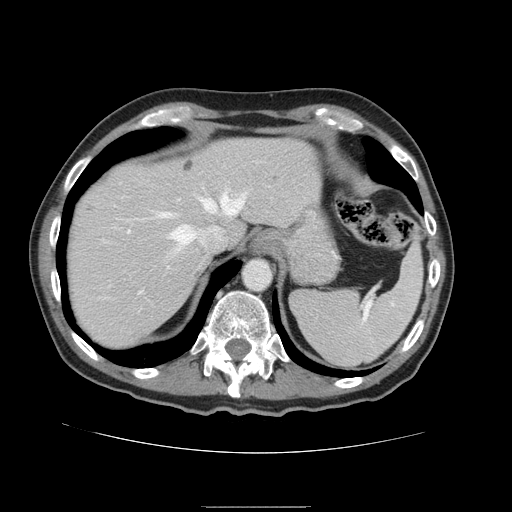
Contrast-enhanced abdominal CT, one axial slice; slice 122 of 168 in the series (ordered by position); soft-tissue window (W 400 / L 40 HU); 512 × 512 image matrix, field of view 386 × 386 mm. Male patient, age 74 years. Case-level facts recorded for this patient, not image findings: diagnosis: colorectal cancer liver metastases, imaged before liver resection; multiple liver metastases: no; largest metastasis: 14.5 cm.
Outlined on this slice (manually delineated by an expert):
- hepatic veins: bounding box (x1, y1, x2, y2) in pixels: (140, 194, 244, 293)
- liver: (67, 139, 322, 350)
- planned liver remnant (the part of the liver to remain after resection): (66, 139, 322, 350)